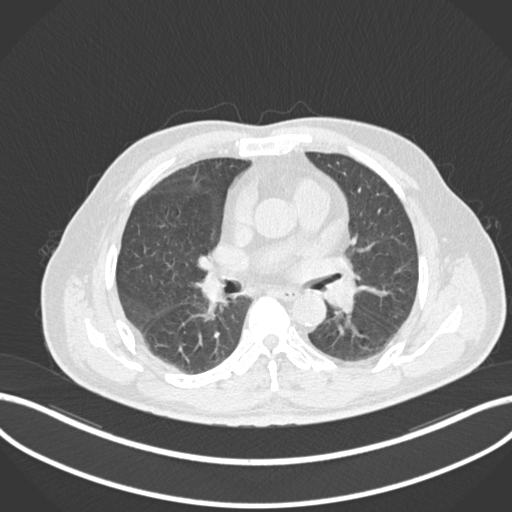
Chest CT, one axial slice; position 74 of 161 along the scan axis; reconstruction kernel B30f; lung window (W 1500 / L -600 HU); 1 mm slice thickness; 512 × 512 image matrix, field of view 400 × 400 mm. Male patient, age 71 years. Case-level facts recorded for this patient, not image findings: clinical TNM (as recorded): T1b N0 M0.
Annotated regions visible in this slice (bounding box drawn by a radiologist):
- lung tumour (recorded histology: squamous cell carcinoma): box from (x=320, y=273) to (x=365, y=313) px